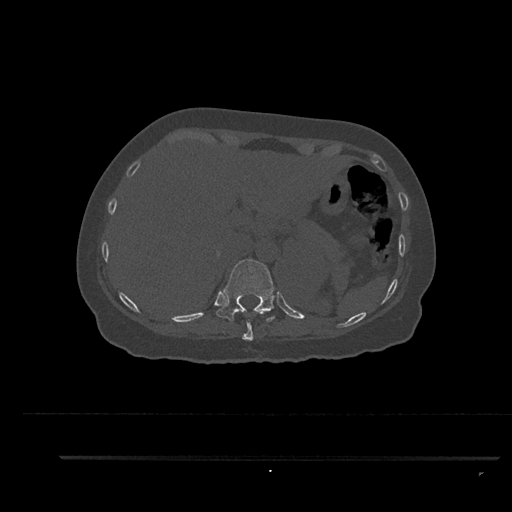
CT including the spine, one axial slice. Slice 330 of 797 in the series (ordered by position). 120 kVp. Bone window (W 1800 / L 400 HU). 0.5 mm slice thickness. 512 × 512 image matrix. Patient: female, 44 years. Case-level facts recorded for this patient, not image findings: primary cancer: renal; vertebrae with lytic lesions (as recorded): L1.
Structures marked on this image (semi-automatic segmentation, software-assisted and operator-edited):
- T10 vertebra: box from (x=242, y=309) to (x=254, y=341) px
- T11 vertebra: (x=216, y=259)–(x=275, y=322)